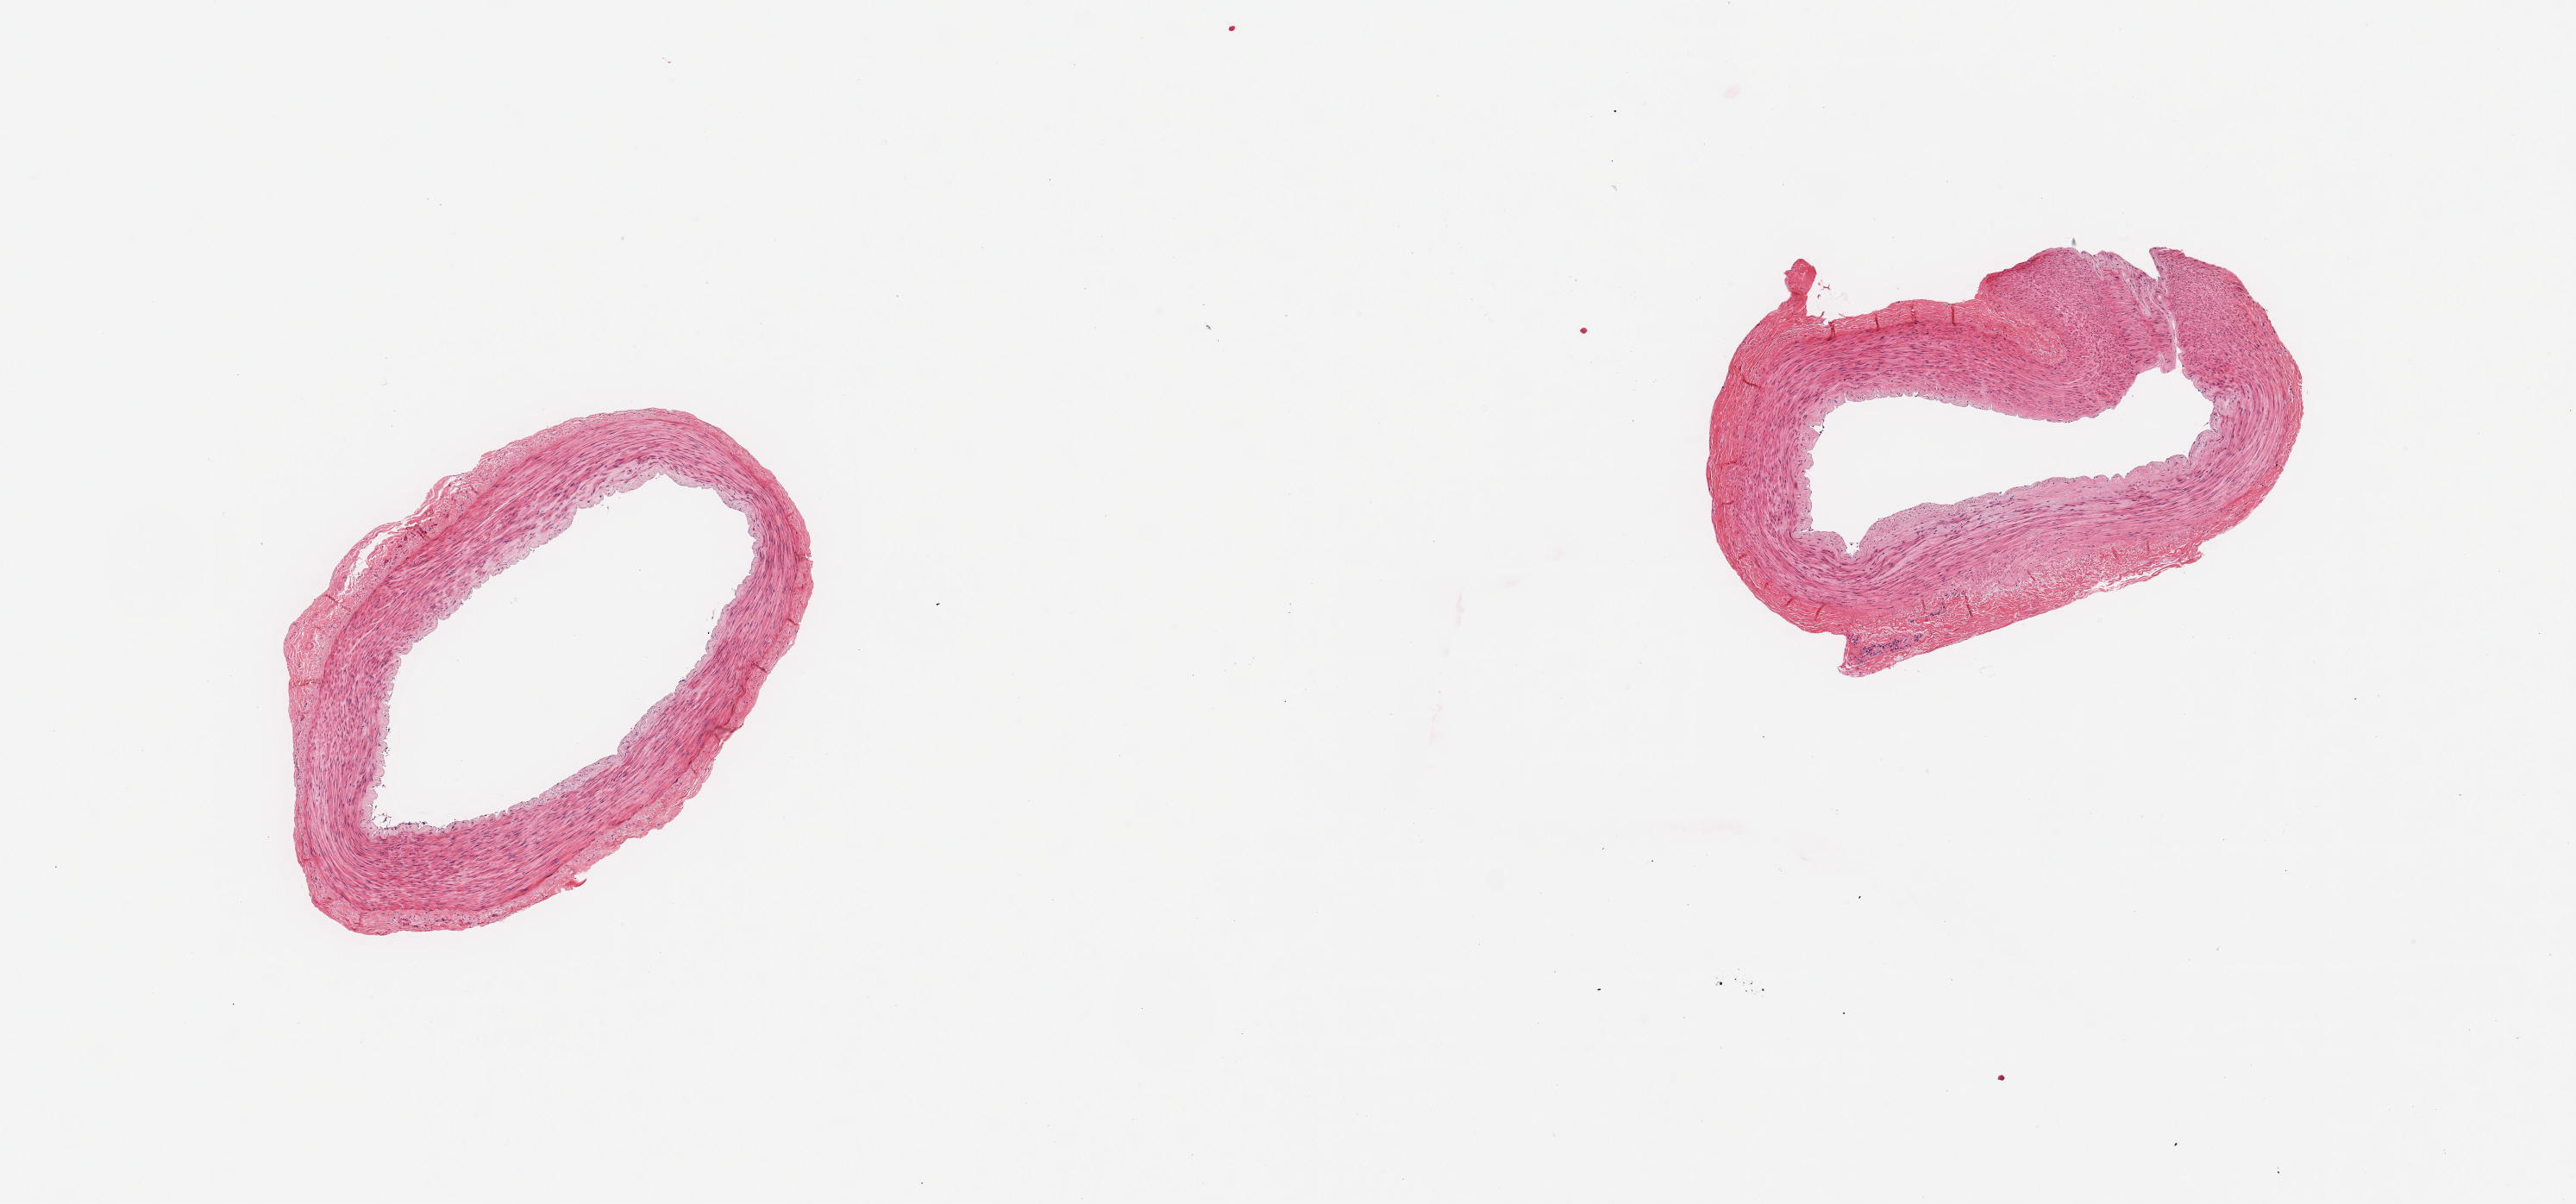
Hematoxylin and eosin (H&E) whole-slide image — shown as a low-resolution overview of the whole scanned area (about 11.8 x 5.5 mm); PAXgene-fixed paraffin-embedded (PFPE) section; sampled site (target tissue): tibial artery; tissue donor sample. Donor: male.
* pathologist's review note for this sample: 2 pieces; thin rim of adherent adventitia